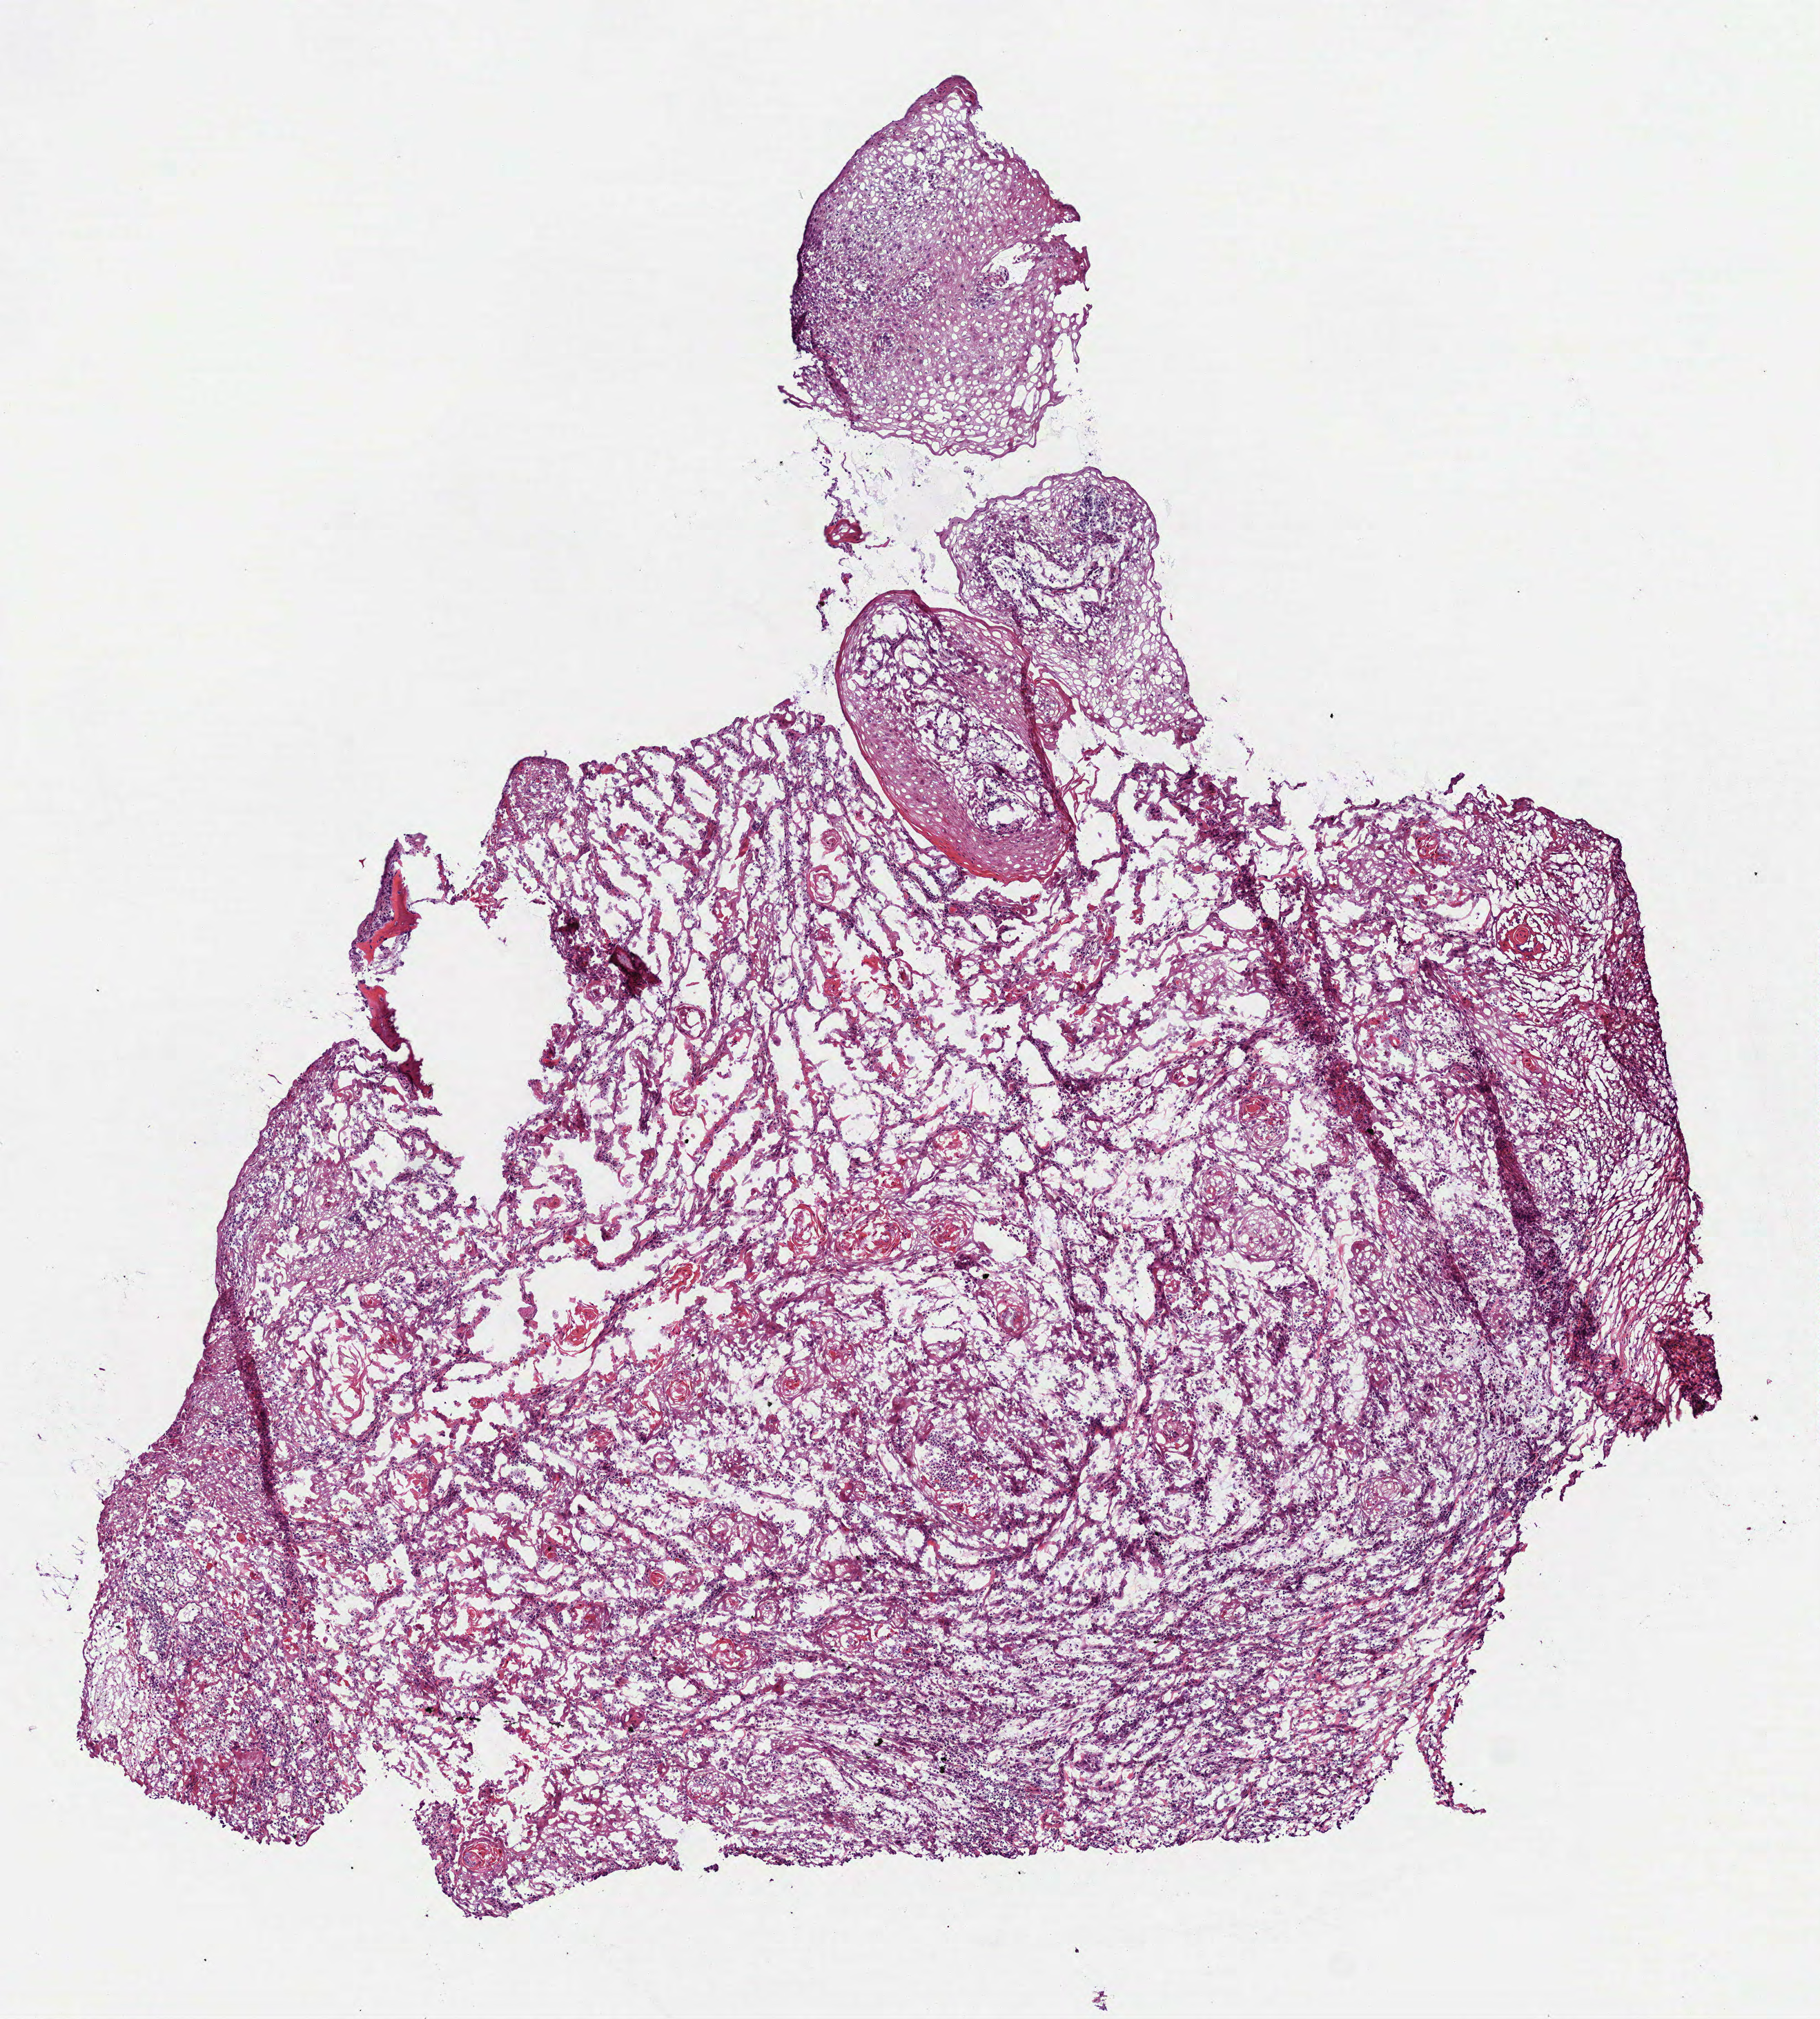
Hematoxylin and eosin (H&E) stained whole-slide image, a low-resolution overview of the entire scanned area, about 5.3 x 5.9 mm, frozen section from the bottom of the tissue portion, primary tumour sample from the head and neck. Patient: female, age at initial diagnosis 74 years. Histologic grade: G3 (poorly differentiated). Composition of this section per pathologist review: tumour cells 85%, tumour nuclei 60%, normal cells 5%, stromal cells 10%, necrosis 0%. Inflammatory infiltration, as recorded: lymphocyte infiltration 30%, monocyte infiltration 0%, neutrophil infiltration 5%.
AJCC pathologic stage: II (7th edition). Histologic diagnosis: Squamous cell carcinoma, NOS (overlapping lesion of lip, oral cavity and pharynx).